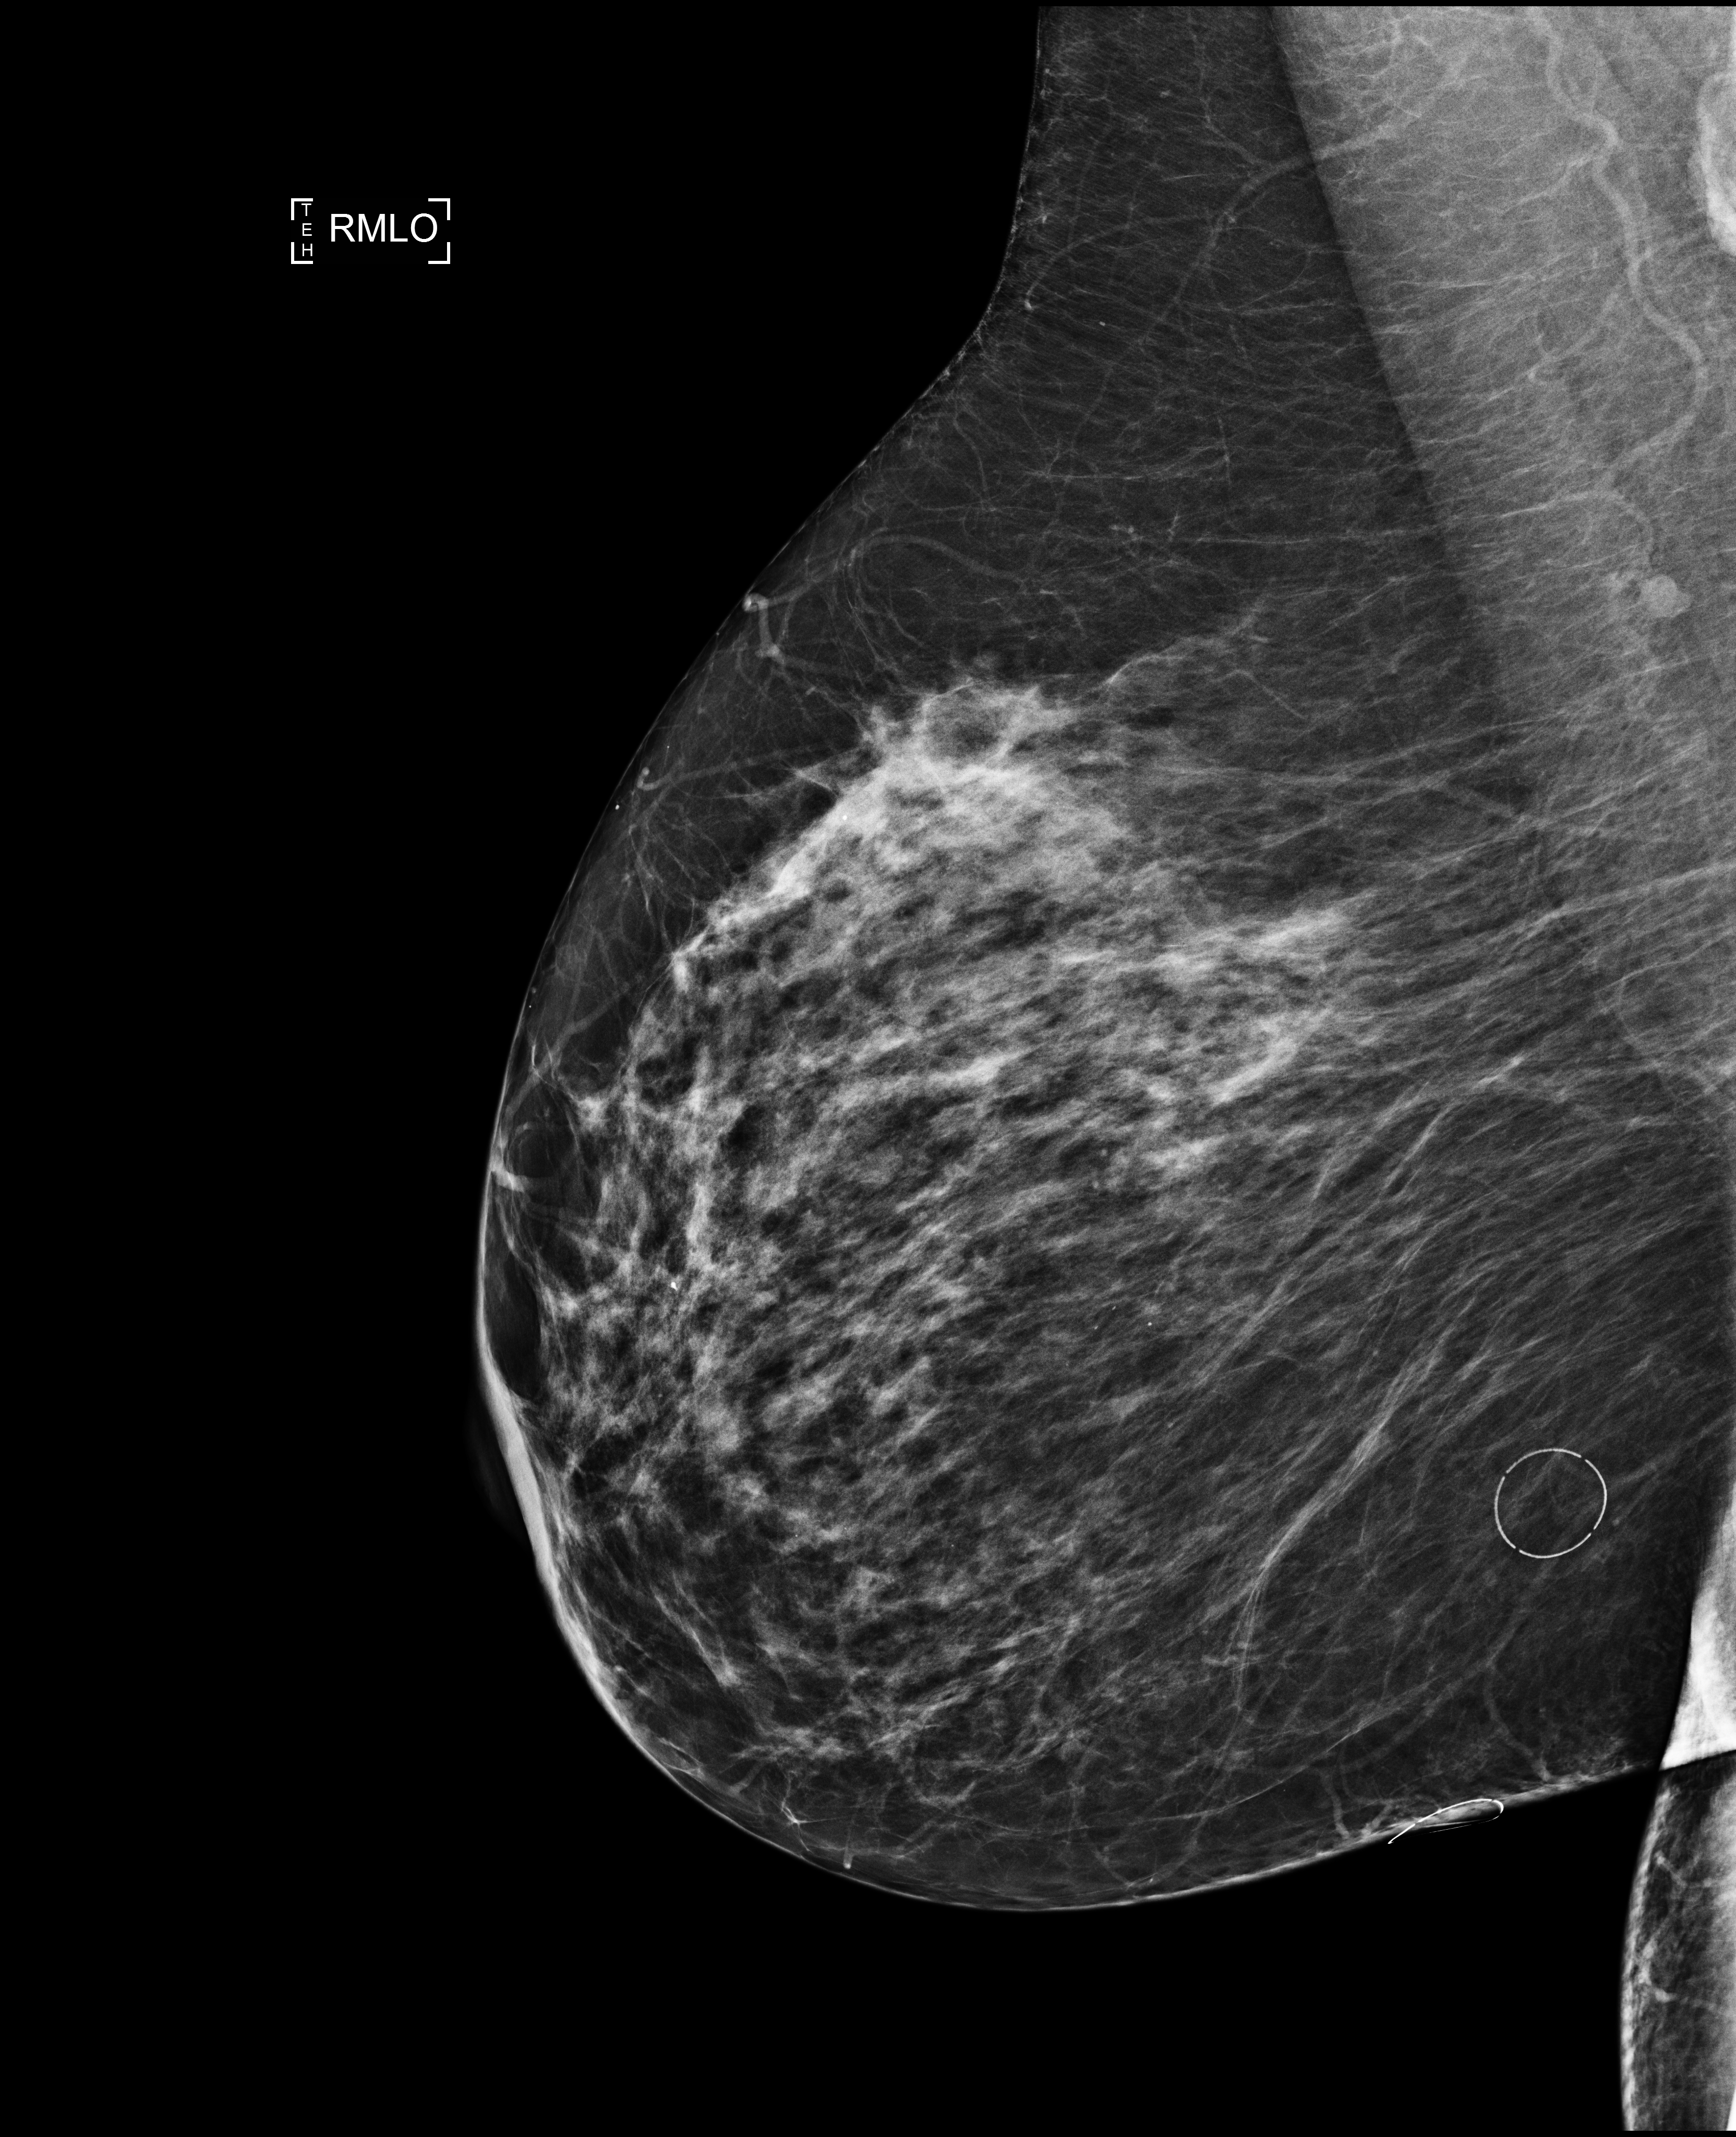
Screening examination; compressed breast thickness 66 mm. Female patient, age 61 years.
Image type: full-field digital mammogram. Breast: right. Projection: medio-lateral oblique projection. BI-RADS breast density category at the screening exam (both breasts, scale 1–4): 3. Final BI-RADS assessment for this screening round (tomosynthesis exam, both breasts): category 2. Recall: recalled for additional imaging after this screen.